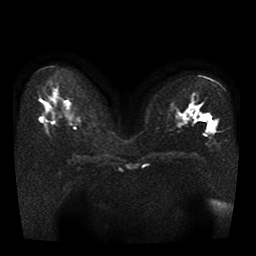
Breast MRI, one axial slice; position 19 of 41 along the scan axis; diffusion-weighted series; image 2 of 4 stored at this slice position (different b-values; order by instance number); 1.5 T; 256 × 256 image matrix, field of view 330 × 330 mm. Female patient.
Annotated regions visible in this slice (expert manual segmentation):
- tumour on diffusion-weighted imaging: bounding box <208,119,213,127> (left, top, right, bottom; pixels)